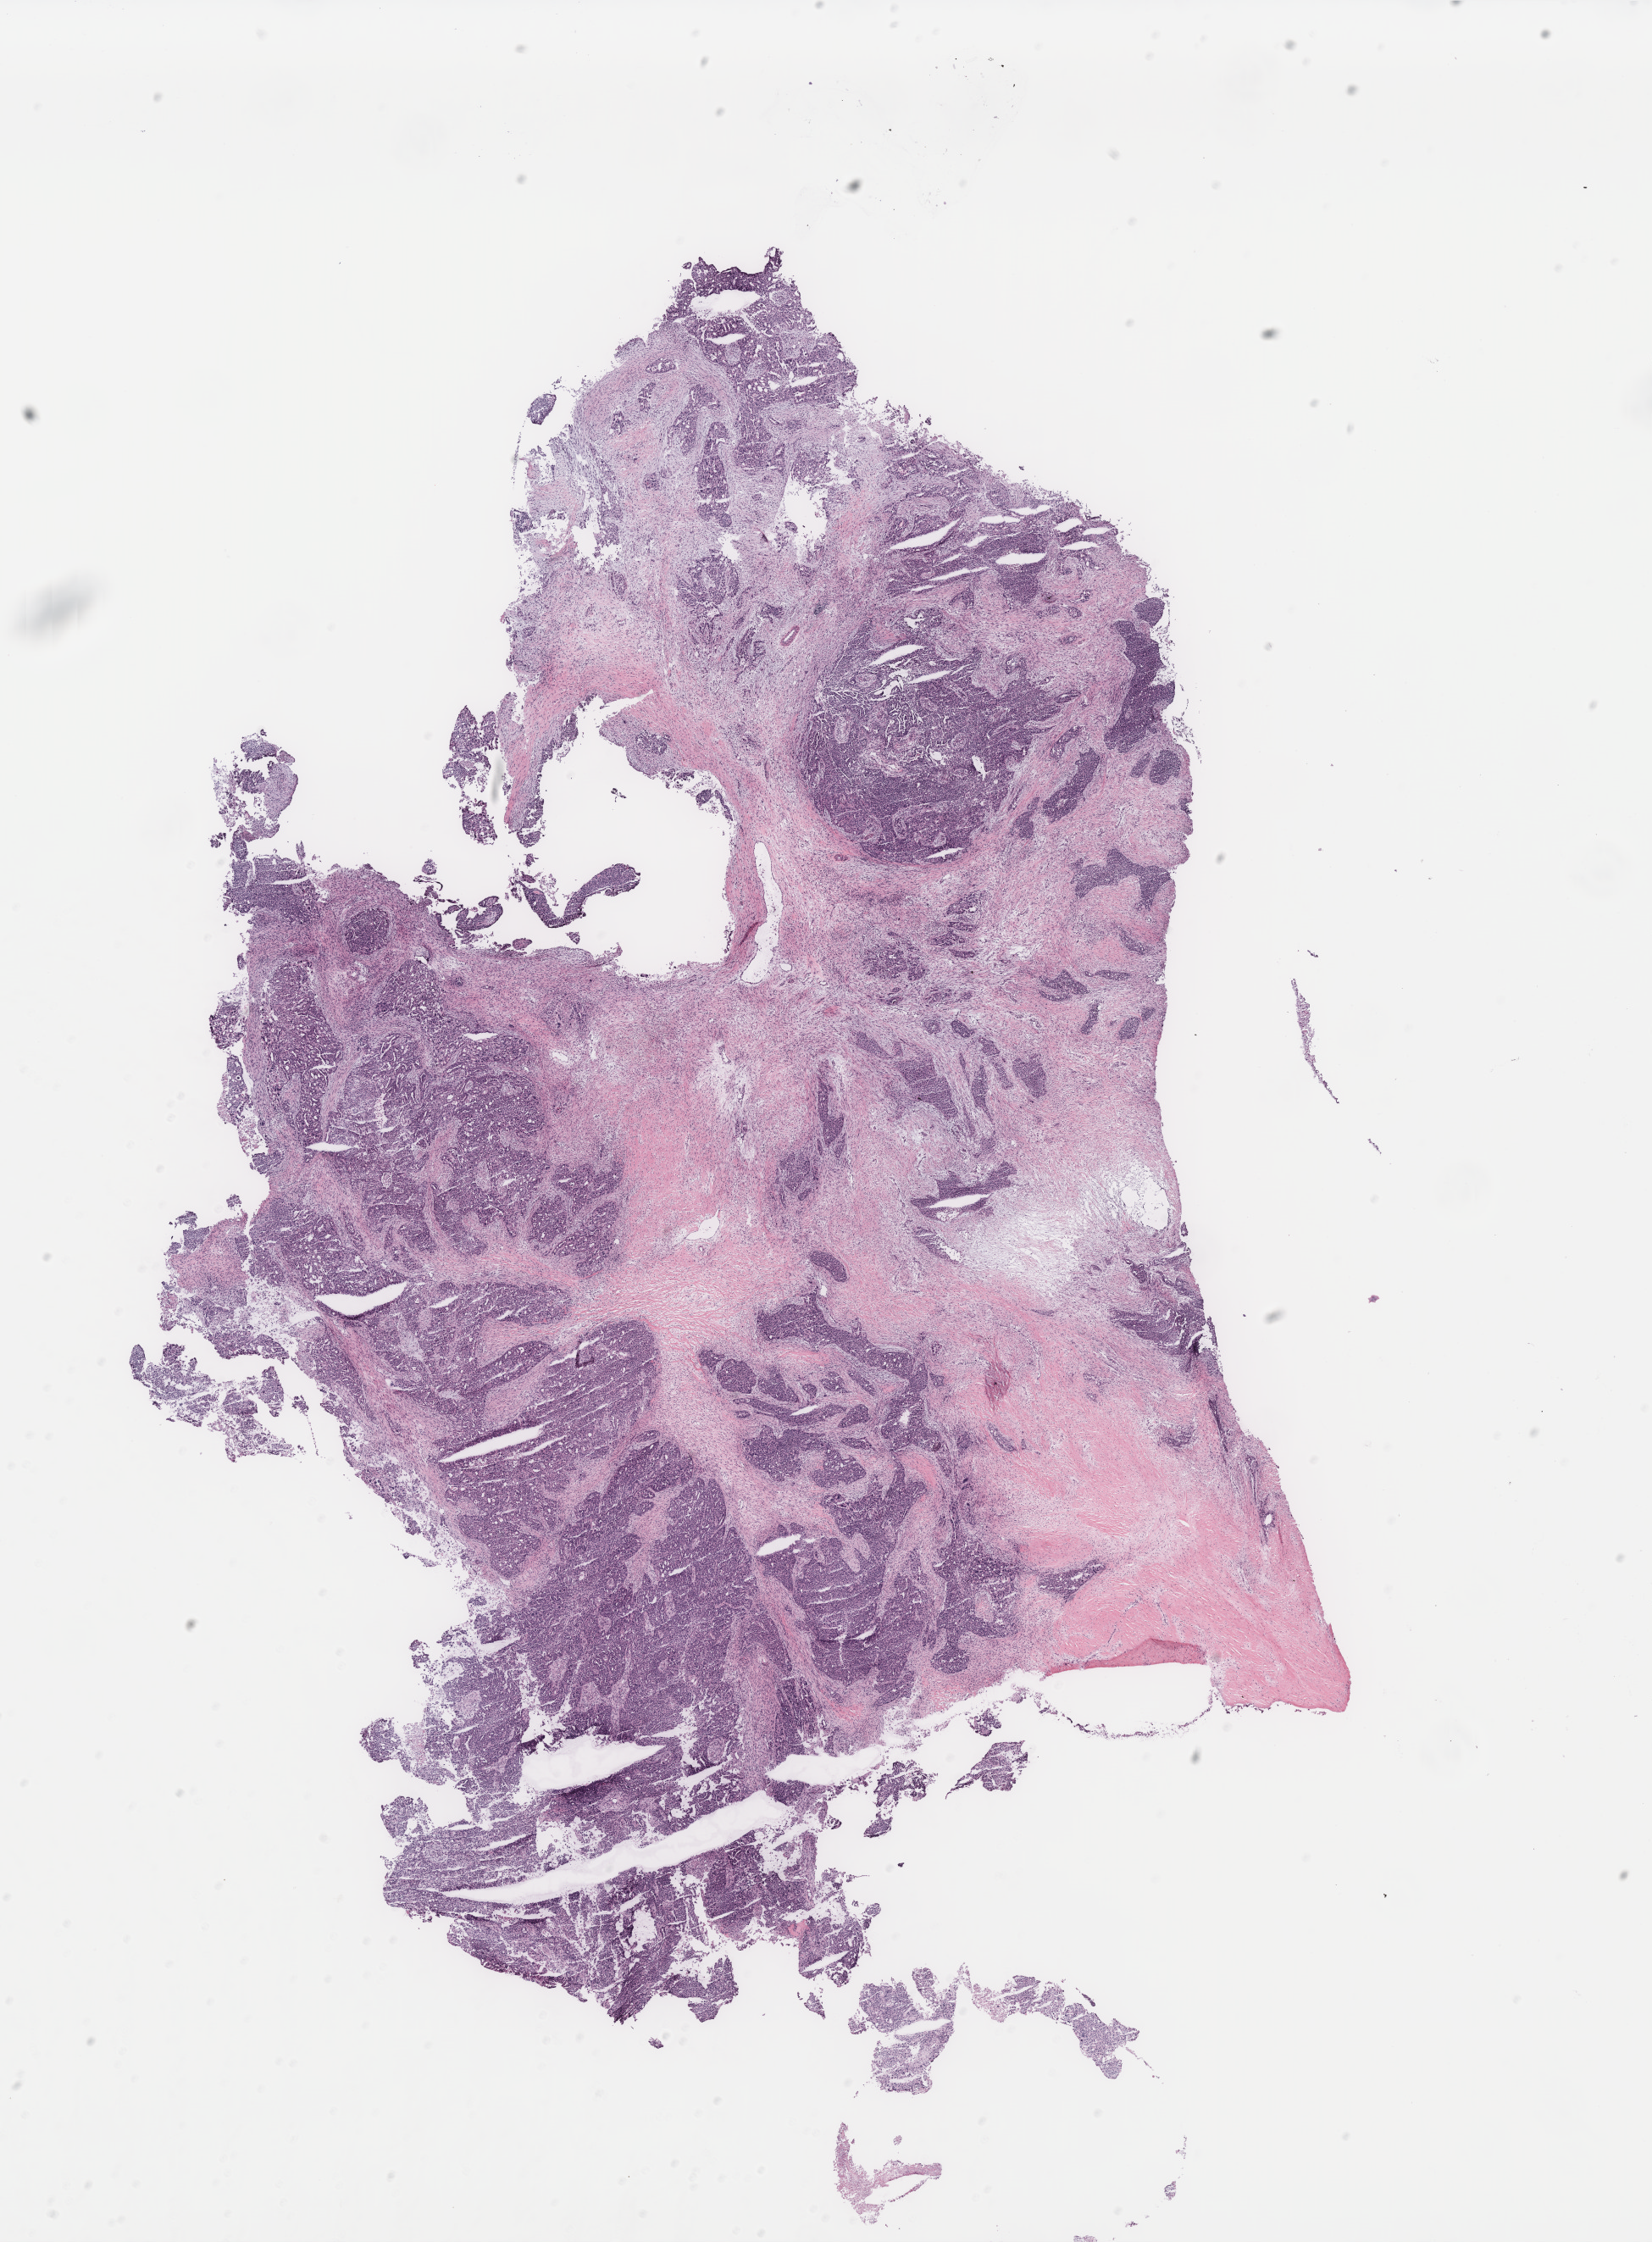
Digitized H&E-stained tissue section (whole slide) — a low-resolution overview of the entire scanned area, about 15.6 x 21.2 mm (slide scanned at 40x), ovary, tumour tissue. Patient: female, age 57 years.
Primary tumour site (as recorded): ovary. Histologic diagnosis: Serous adenocarcinoma, NOS.